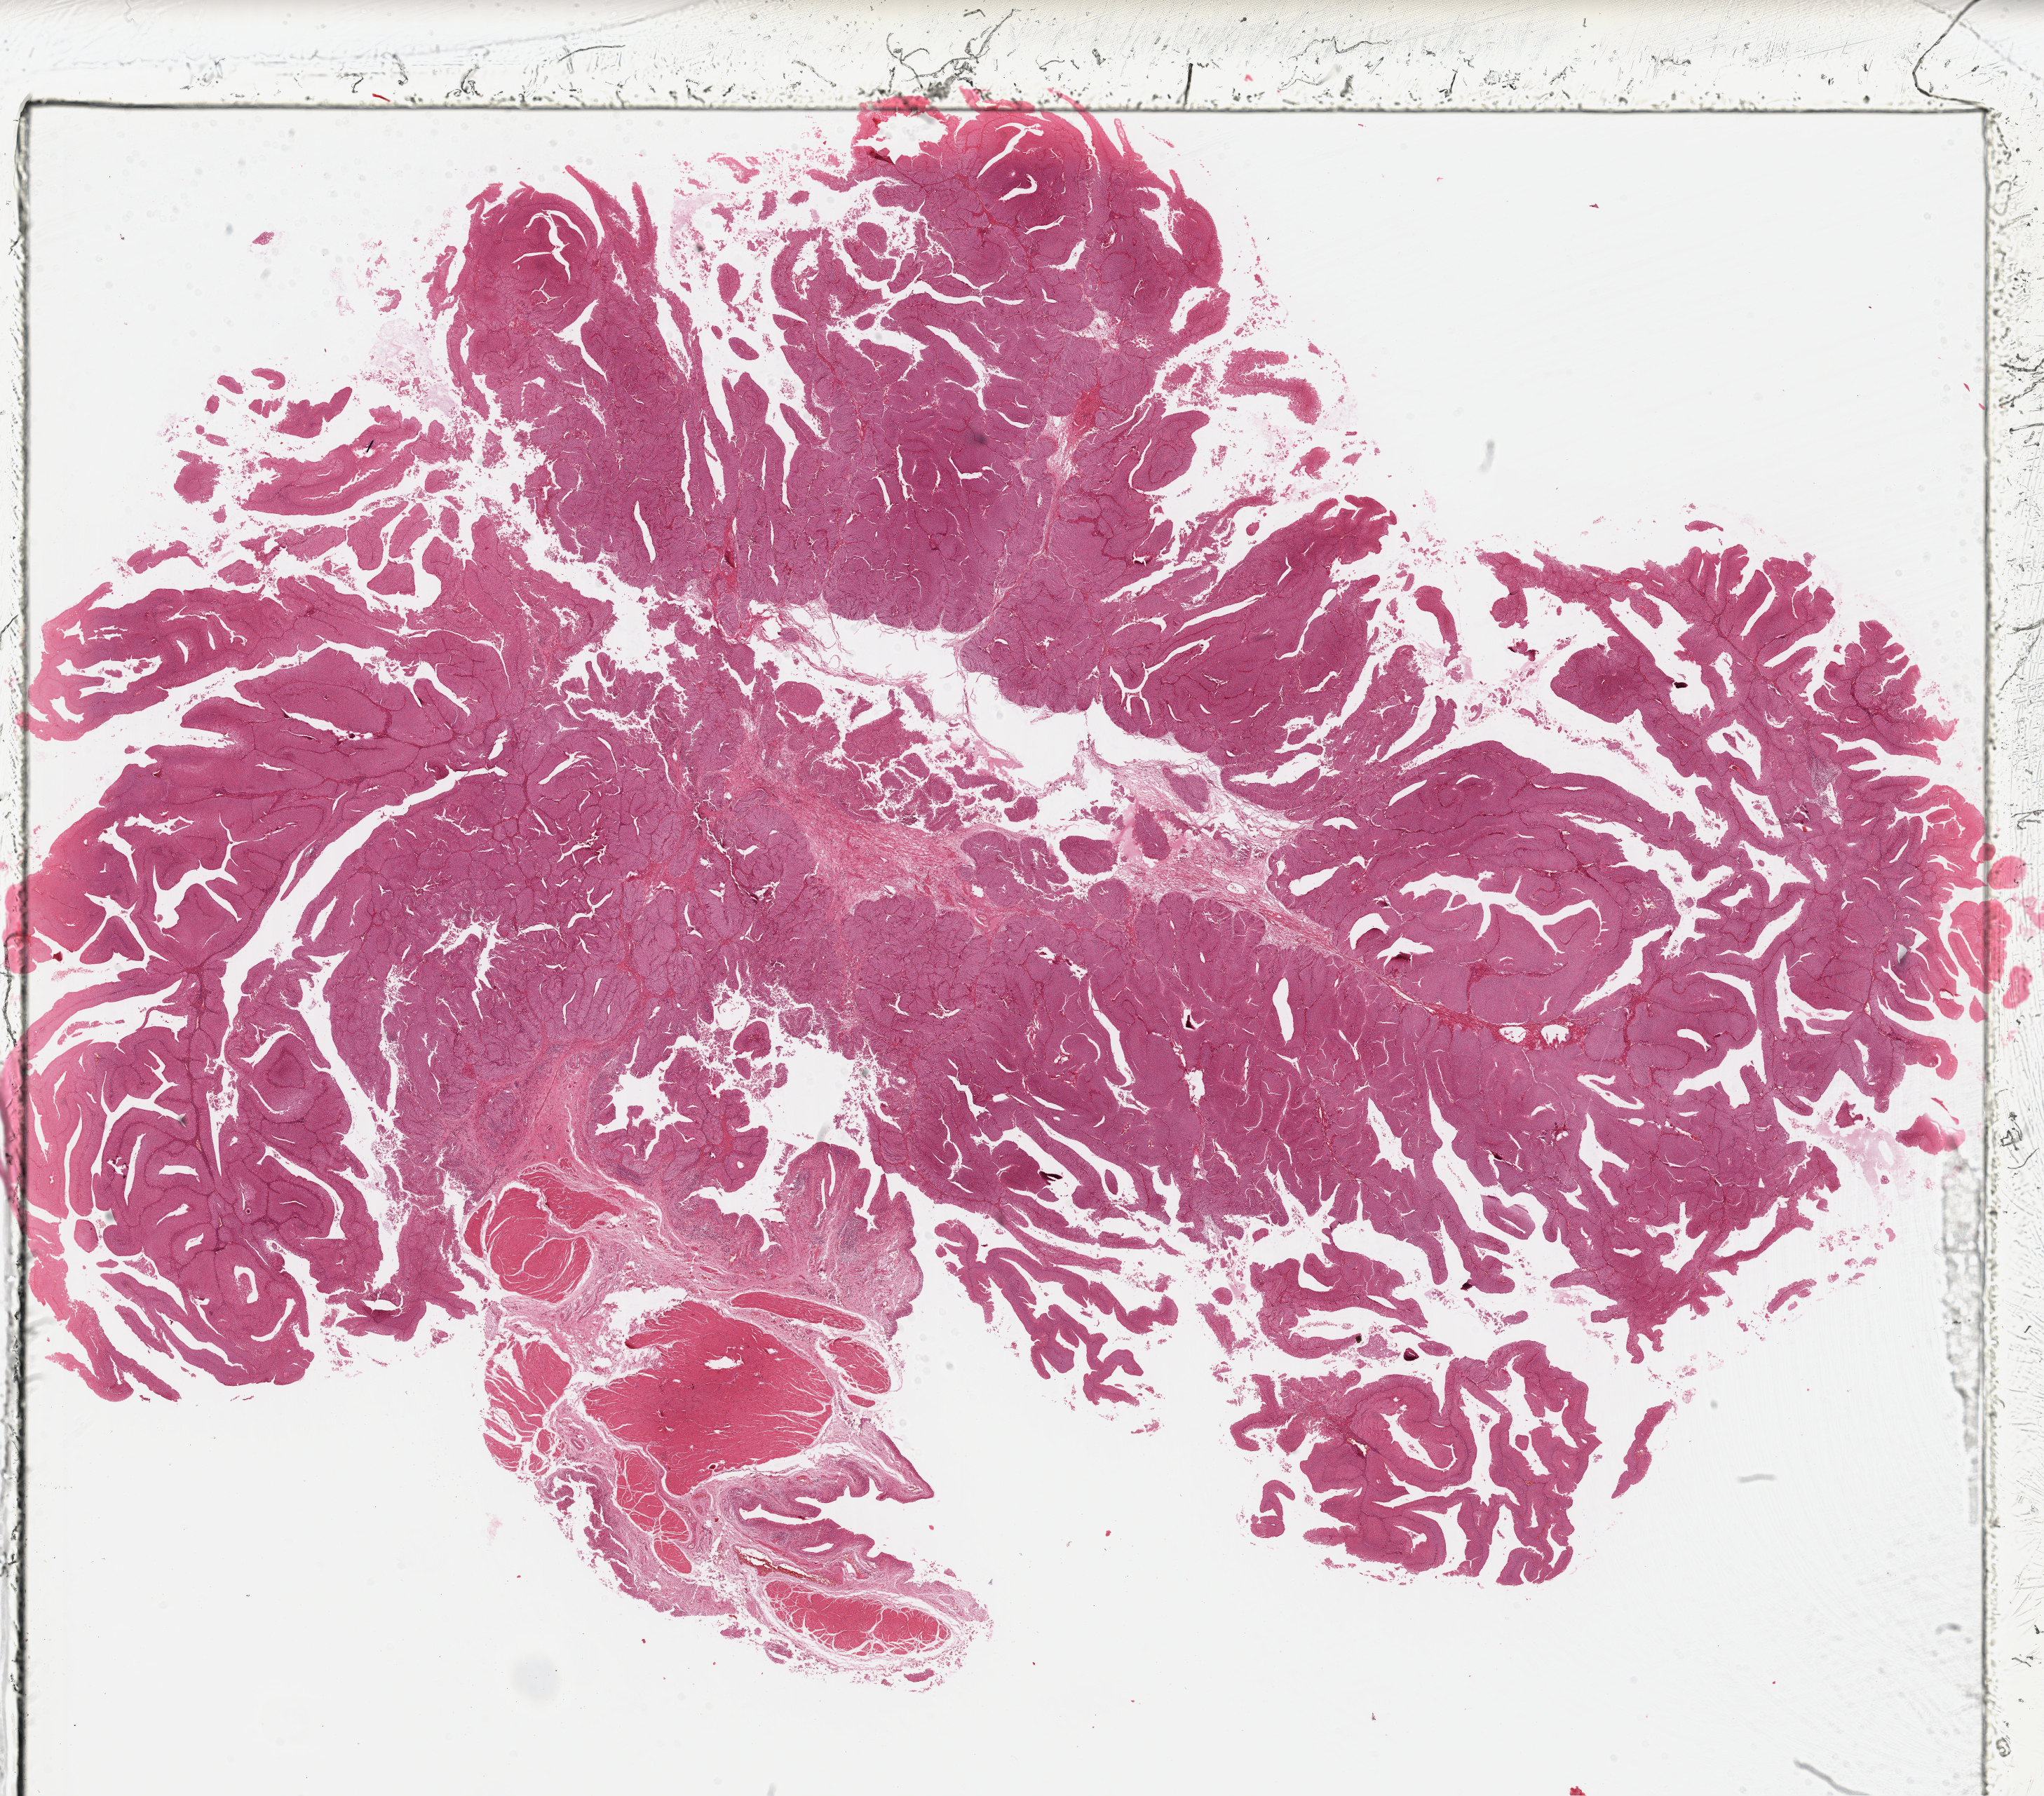
Whole-slide histology image, H&E-stained, low-resolution overview of the scanned area, about 22.9 x 20.1 mm, FFPE section, primary tumour sample from the bladder. Male patient; age at initial diagnosis 41 years. Histologic grade: low grade.
• AJCC pathologic stage: II (7th edition)
• histologic diagnosis: Papillary transitional cell carcinoma